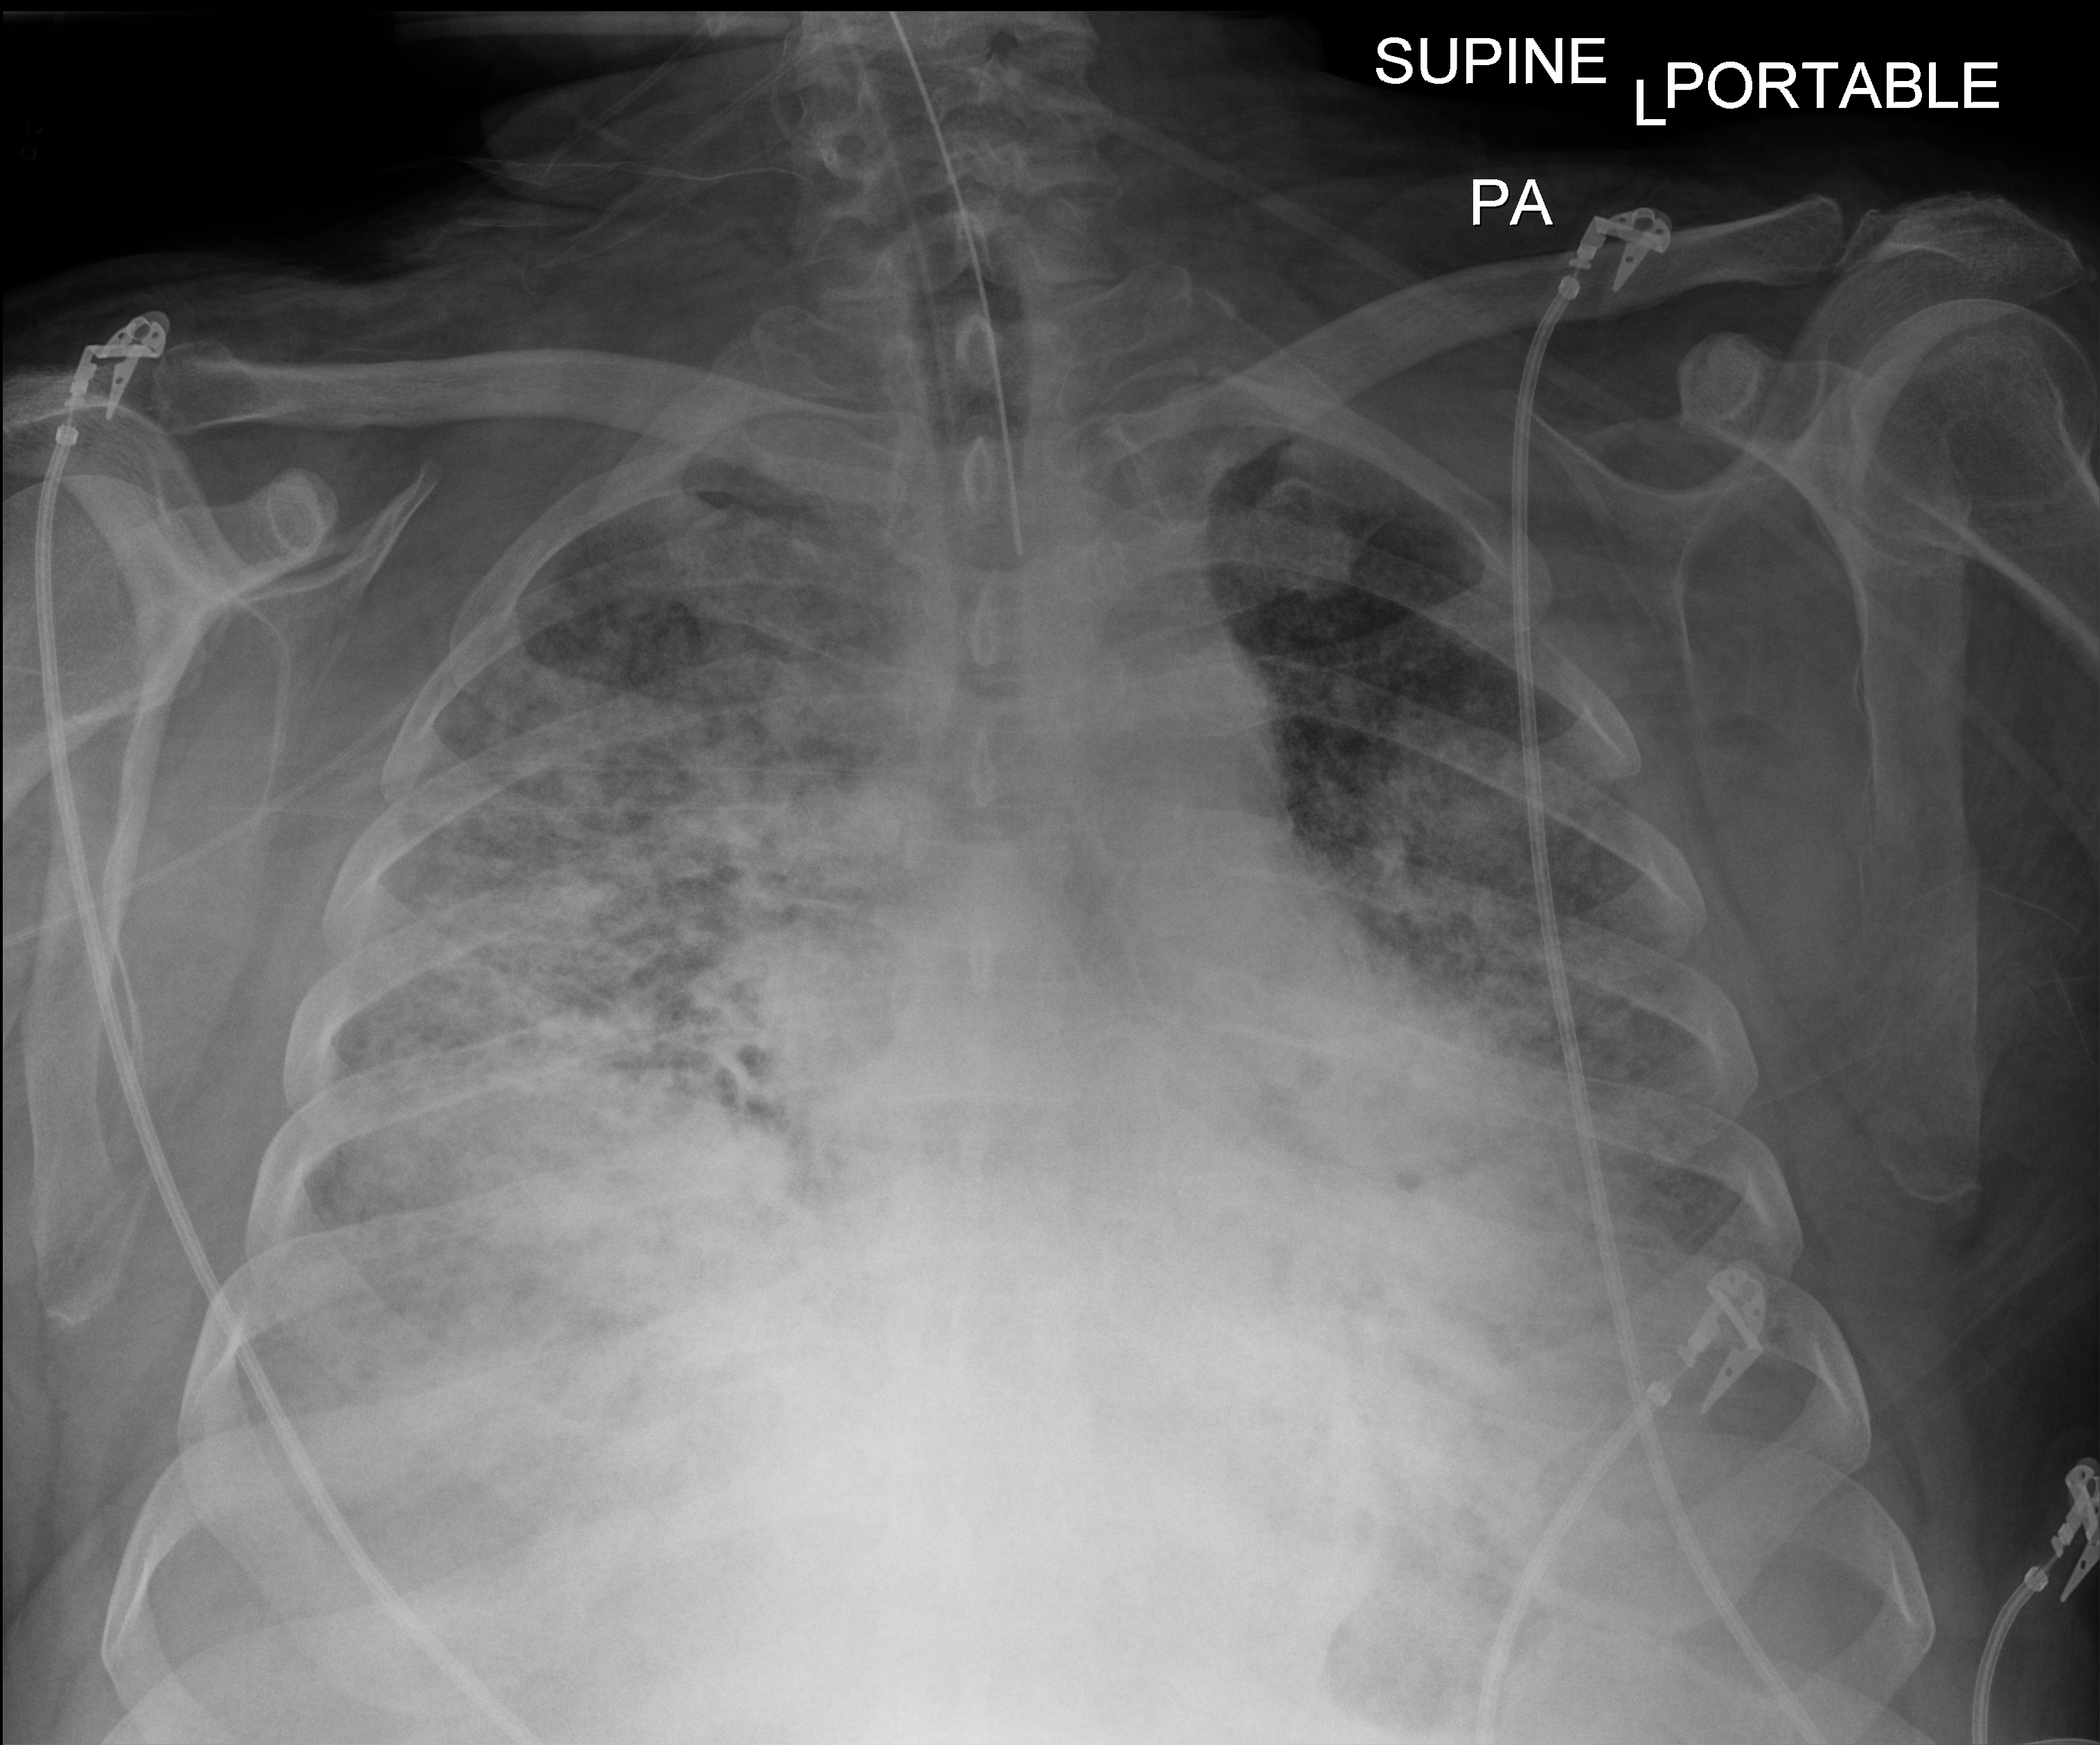
Bedside chest radiograph (digital radiography); posteroanterior (PA) projection. Patient hospitalised with COVID-19; male, aged 60–74 years.
Hospital-stay facts (about this admission, not read from this image; timing relative to this image not recorded): admitted to intensive care during this hospital stay: yes.